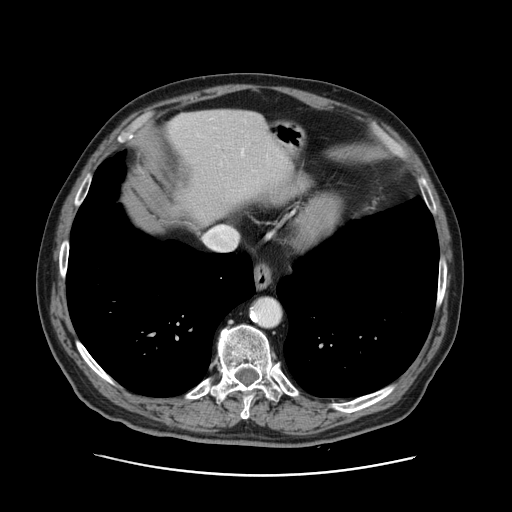
Contrast-enhanced abdominal CT, one axial slice. Slice 116 of 141 in the series (ordered by position). 120 kVp. Intravenous contrast given. Soft-tissue window (W 400 / L 40 HU). 2.5 mm slice thickness. 512 × 512 image matrix. Male patient, age 72 years. From the clinical record (not read from this slice): diagnosis: colorectal cancer liver metastases, imaged before liver resection; multiple liver metastases: yes; largest metastasis: 5.4 cm; disease in both lobes: yes.
Outlined on this slice (manually delineated by an expert):
- liver: bounding box (x1, y1, x2, y2) in pixels: (167, 109, 288, 224)
- planned liver remnant (the part of the liver to remain after resection): (167, 109, 289, 224)